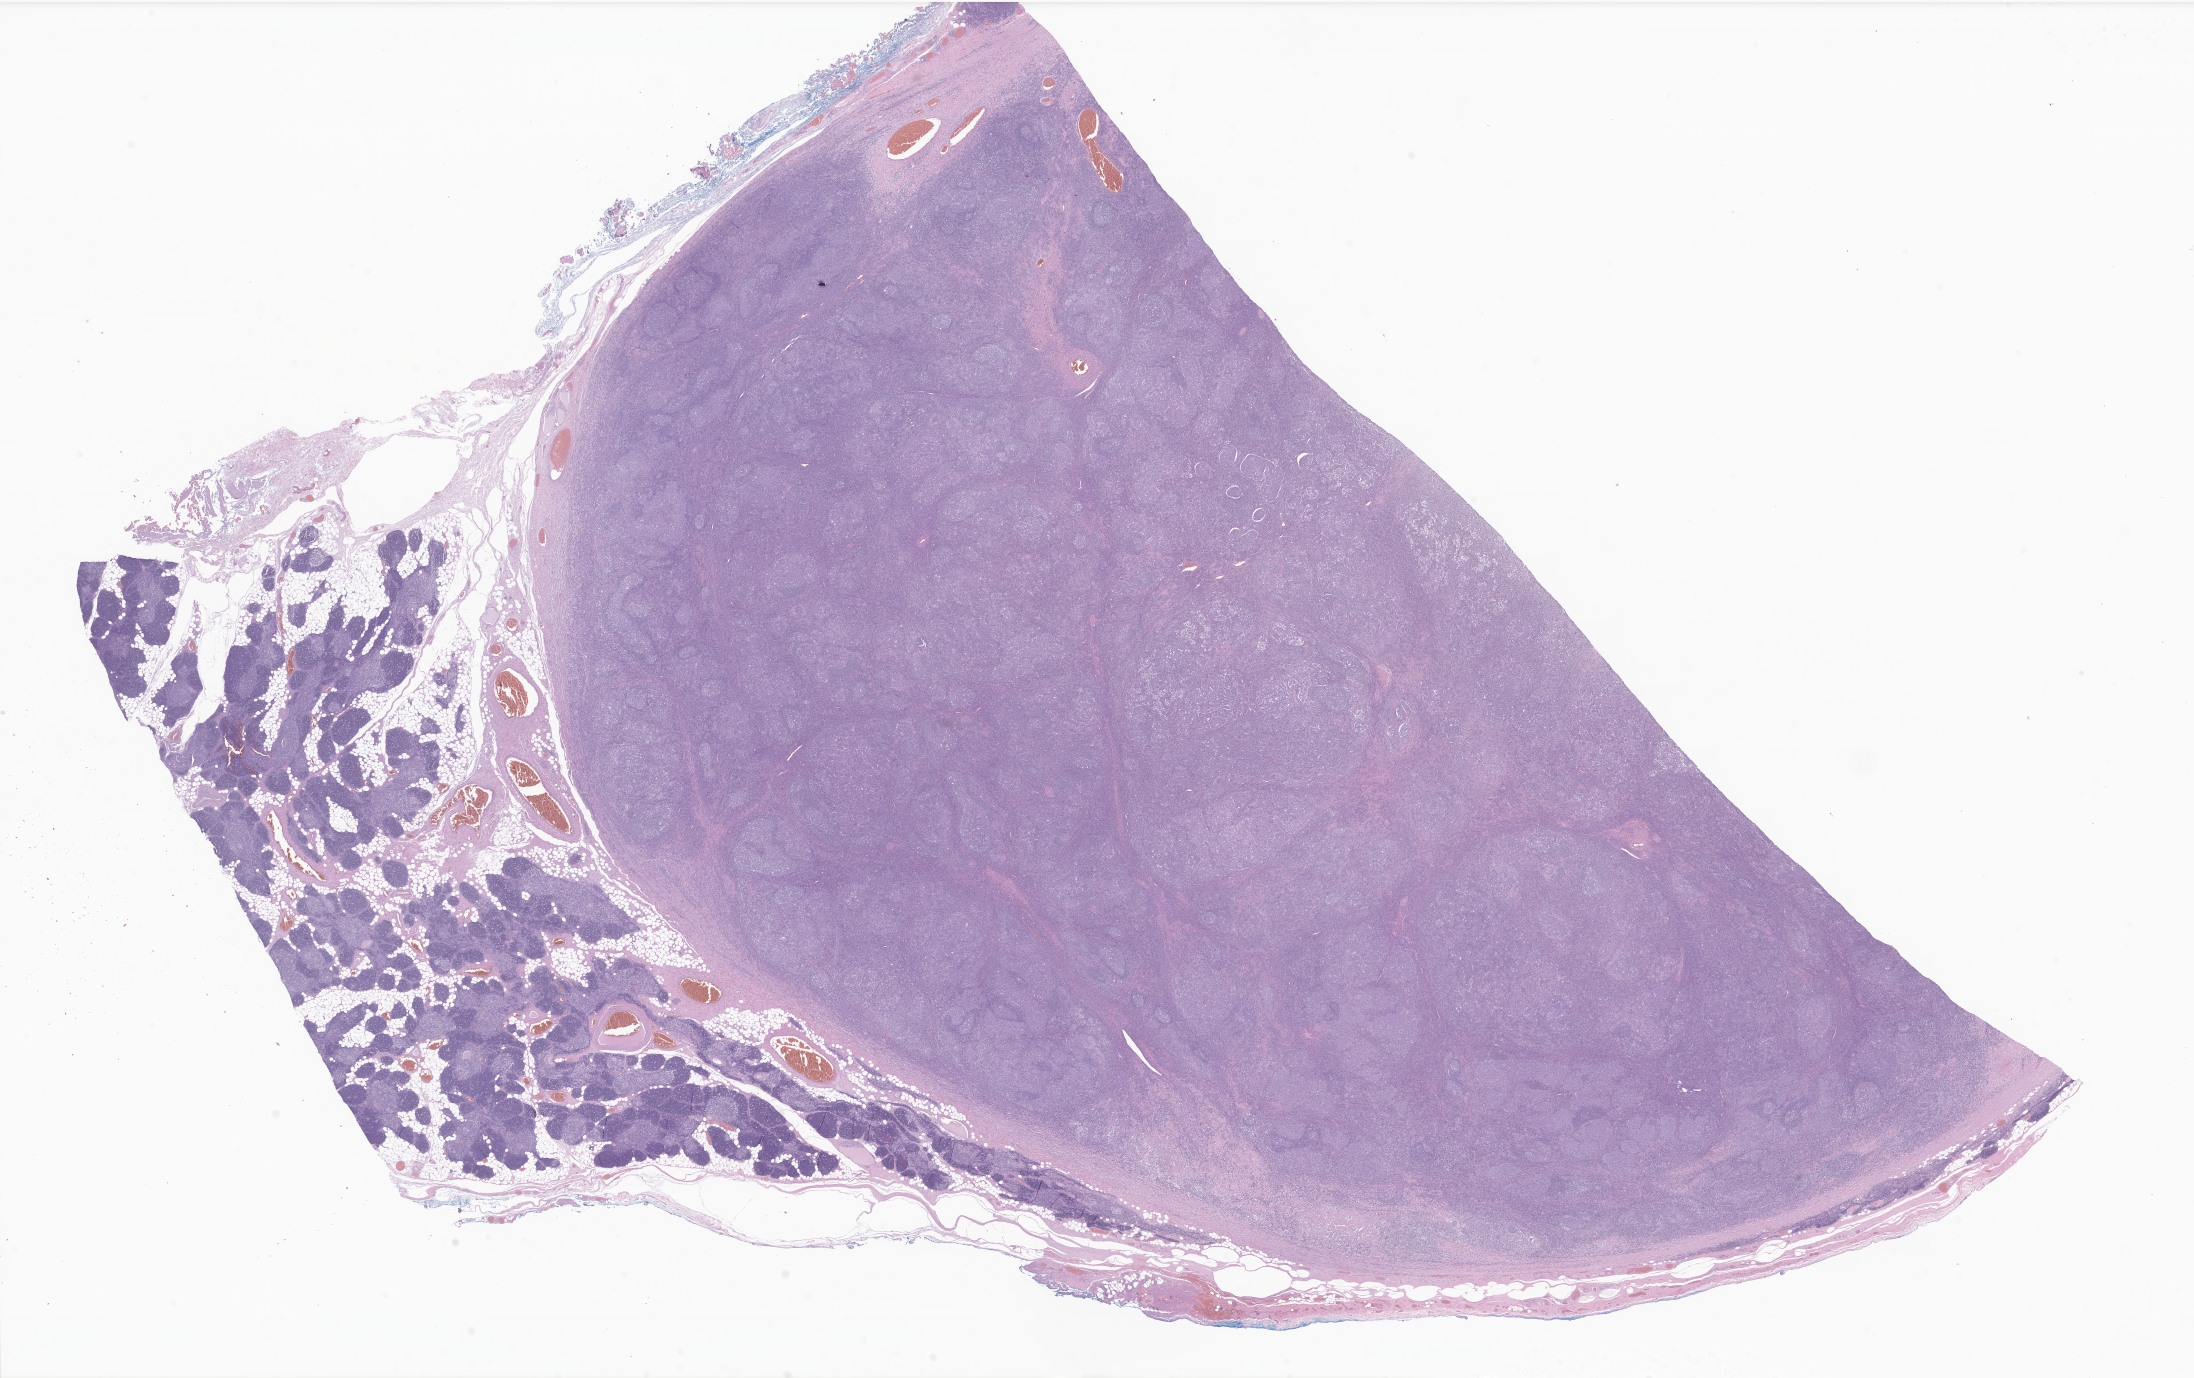
Hematoxylin and eosin (H&E) whole-slide image of tumor tissue from the anterior mediastinum, whole scanned area (about 37.0 x 23.2 mm) shown as a low-resolution overview. Formalin-fixed, paraffin-embedded (FFPE) tissue. Female patient, age 208 months (17 years 4 months).
* diagnosis (ICD-O-3 morphology term): Thymic carcinoma, NOS